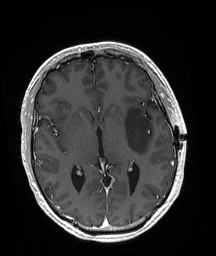
Brain MRI from a brain-tumour surgery series, one axial slice; slice 101 of 192 in the series (ordered by position); T1-weighted post-contrast; 1 mm slice thickness; 216 × 256 image matrix, field of view 211 × 250 mm. From the clinical record (not read from this slice): histopathology: Astrocytoma; WHO grade: 3; IDH mutation: yes.
Structures marked on this image (manually delineated by an expert):
- tumour: bounding box <124,107,152,154> (left, top, right, bottom; pixels)